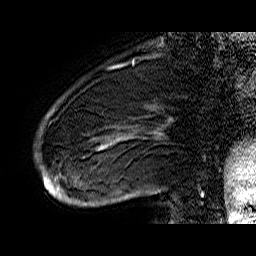
Breast MRI (dynamic contrast-enhanced), one sagittal slice. Position 11 of 60 along the scan axis. Dynamic contrast-enhanced series, time point 2 of 6 at this slice position (early post-contrast). 1.5 T. TE 6.4 ms, TR 32.9 ms. 256 × 256 image matrix, field of view 200 × 200 mm. Female patient. Case-level facts recorded for this patient, not image findings: setting: breast cancer imaged before/during neoadjuvant chemotherapy; receptor status: HR-positive, HER2-negative.
Outlined on this slice (semi-automatic segmentation, software-assisted and operator-edited):
- analysis volume of interest (the breast-tissue region the enhancement analysis was run in; not a lesion): bounding box (x1, y1, x2, y2) in pixels: (42, 75, 176, 206)
- tumour enhancement mask (voxels above the 100 % enhancement threshold inside the analysis volume of interest): (42, 111, 124, 201)